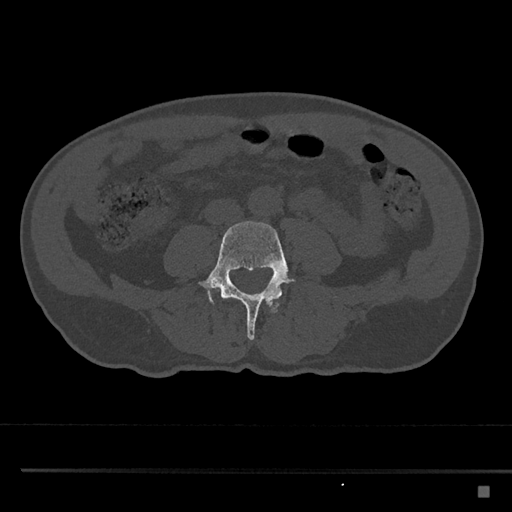
CT including the spine, one axial slice; slice 637 of 797 in the series (ordered by position); bone window (W 1800 / L 400 HU); 0.5 mm slice thickness; 512 × 512 image matrix. Patient: male, 59 years. Case-level facts recorded for this patient, not image findings: primary cancer: prostate.
Outlined on this slice (semi-automatically segmented with operator editing):
- L3 vertebra: bounding box (x1, y1, x2, y2) in pixels: (224, 296, 281, 313)
- L4 vertebra: (199, 221, 294, 341)
- L5 vertebra: (206, 287, 214, 304)